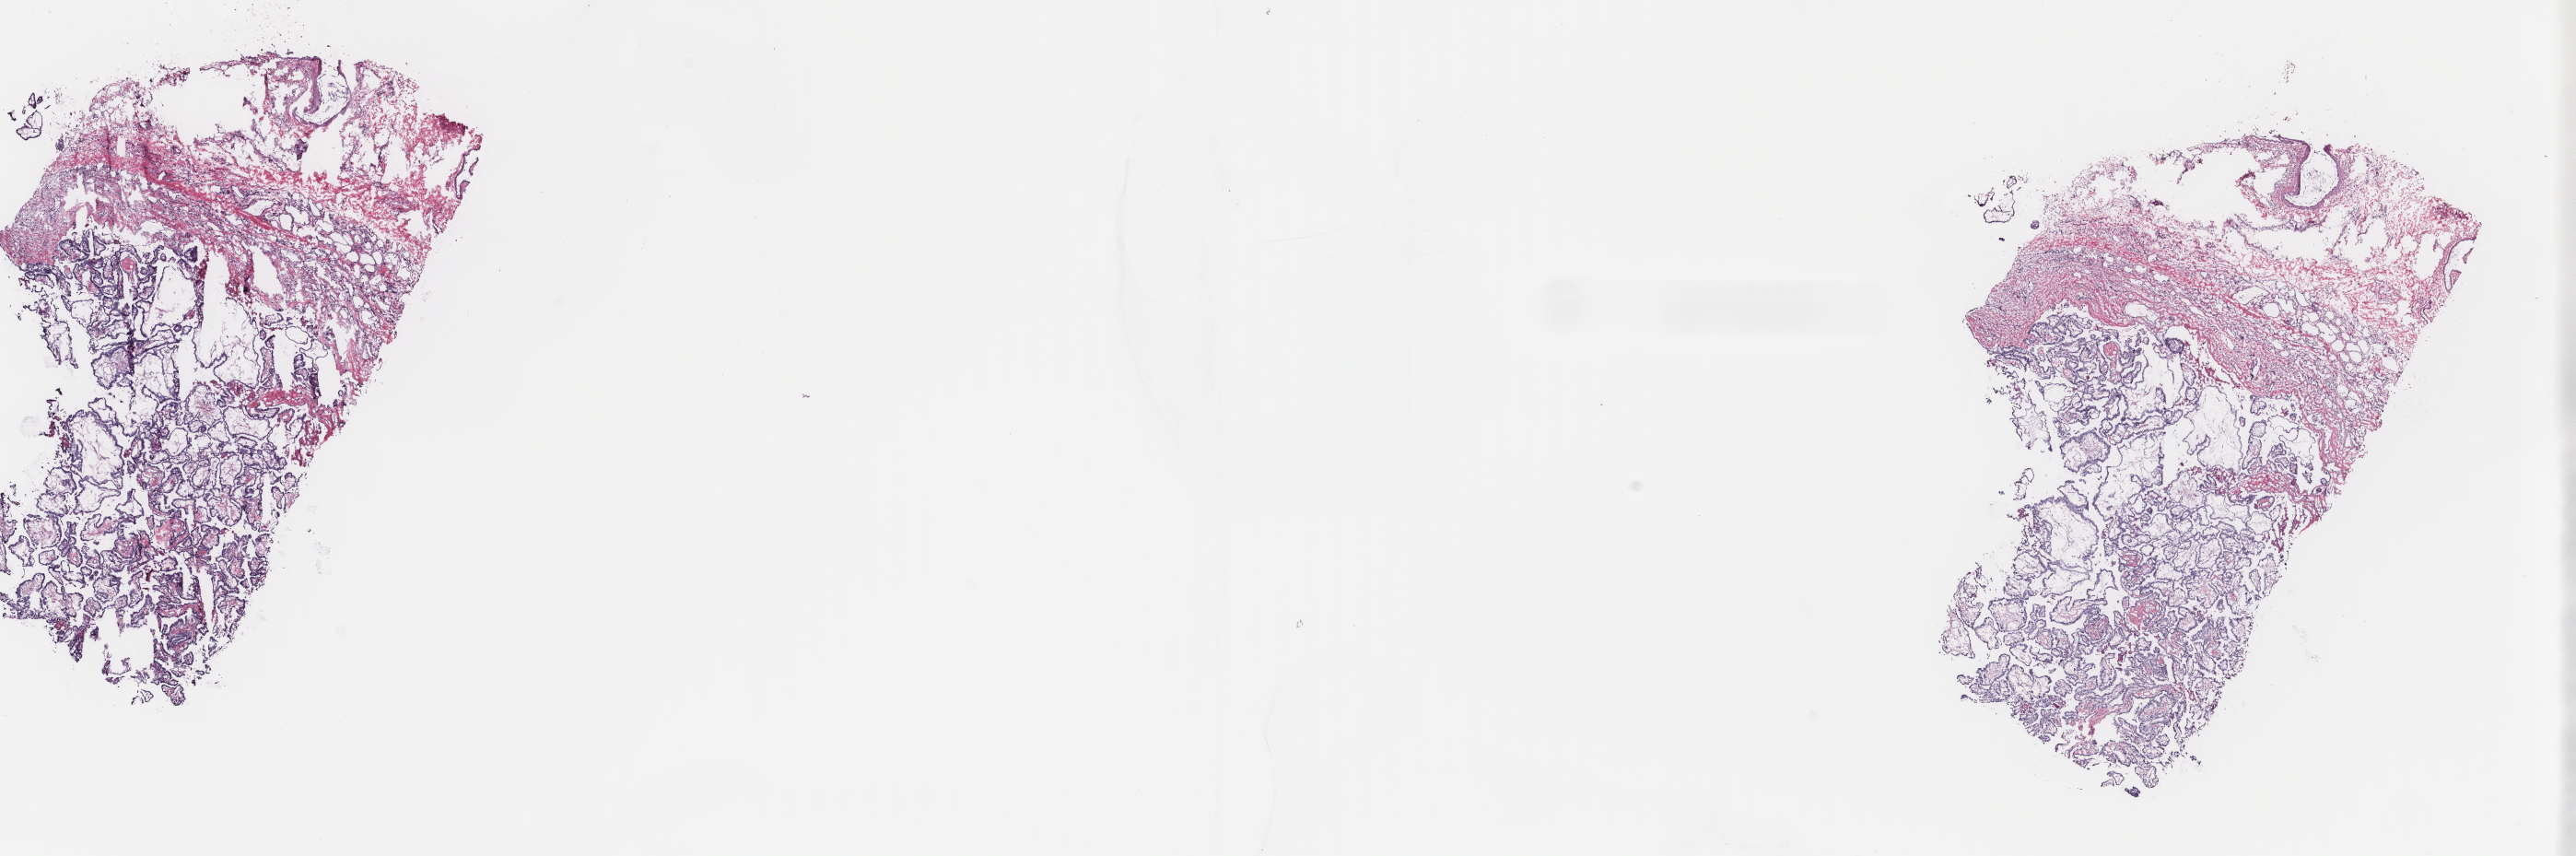
H&E whole-slide image — whole scanned area (about 22.2 x 7.4 mm, slide scanned at 40x) shown as a low-resolution overview. Frozen section. Thyroid, primary tumour sample. Female patient; age at initial diagnosis 31 years. Pathologist review of this section (percent, as recorded): tumour cells 80%, tumour nuclei 85%, normal cells 18%, stromal cells 0%, necrosis 2%. Inflammatory infiltration, as recorded: lymphocyte infiltration 2%, monocyte infiltration 0%, neutrophil infiltration 0%.
AJCC pathologic stage: I. Pathologic diagnosis: Papillary adenocarcinoma, NOS (thyroid gland). TNM: T2 N1a MX.